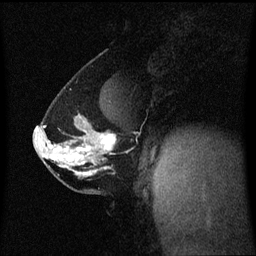
Breast MRI (dynamic contrast-enhanced), one sagittal slice. Slice 35 of 60 in the series (ordered by position). Dynamic contrast-enhanced series, image 2 of 3 at this slice position (ordered by acquisition). 1.5 T. TE 4.2 ms, TR 8.4 ms. 2 mm slice thickness. 256 × 256 image matrix, field of view 210 × 210 mm. Female patient, age 40 years. Case-level facts recorded for this patient, not image findings: setting: breast cancer imaged before/during neoadjuvant chemotherapy; receptor status: triple-negative.
Outlined on this slice (semi-automatically segmented with operator editing):
- analysis volume of interest (the breast-tissue region the enhancement analysis was run in; not a lesion): box from (x=34, y=112) to (x=117, y=188) px
- tumour enhancement mask (voxels above the 70 % enhancement threshold inside the analysis volume of interest): (x=36, y=129)–(x=117, y=161)